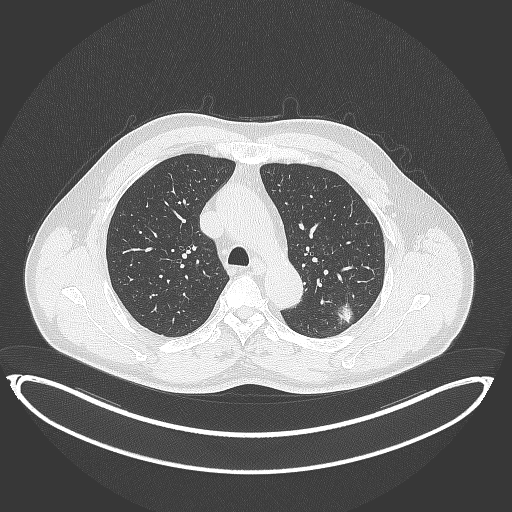
Chest CT, one axial slice. Slice 258 of 399 in the series (ordered by position). 120 kVp. Lung window (W 1500 / L -600 HU). 512 × 512 image matrix. Patient: male, 58 years. From the clinical record (not read from this slice): clinical TNM (as recorded): T1c N0 M0; histopathological grade: G1-2.
Structures marked on this image (rectangle marked by the reading radiologist):
- lung tumour (recorded histology: adenocarcinoma): bounding box [x1, y1, x2, y2] px = [334, 298, 362, 332]